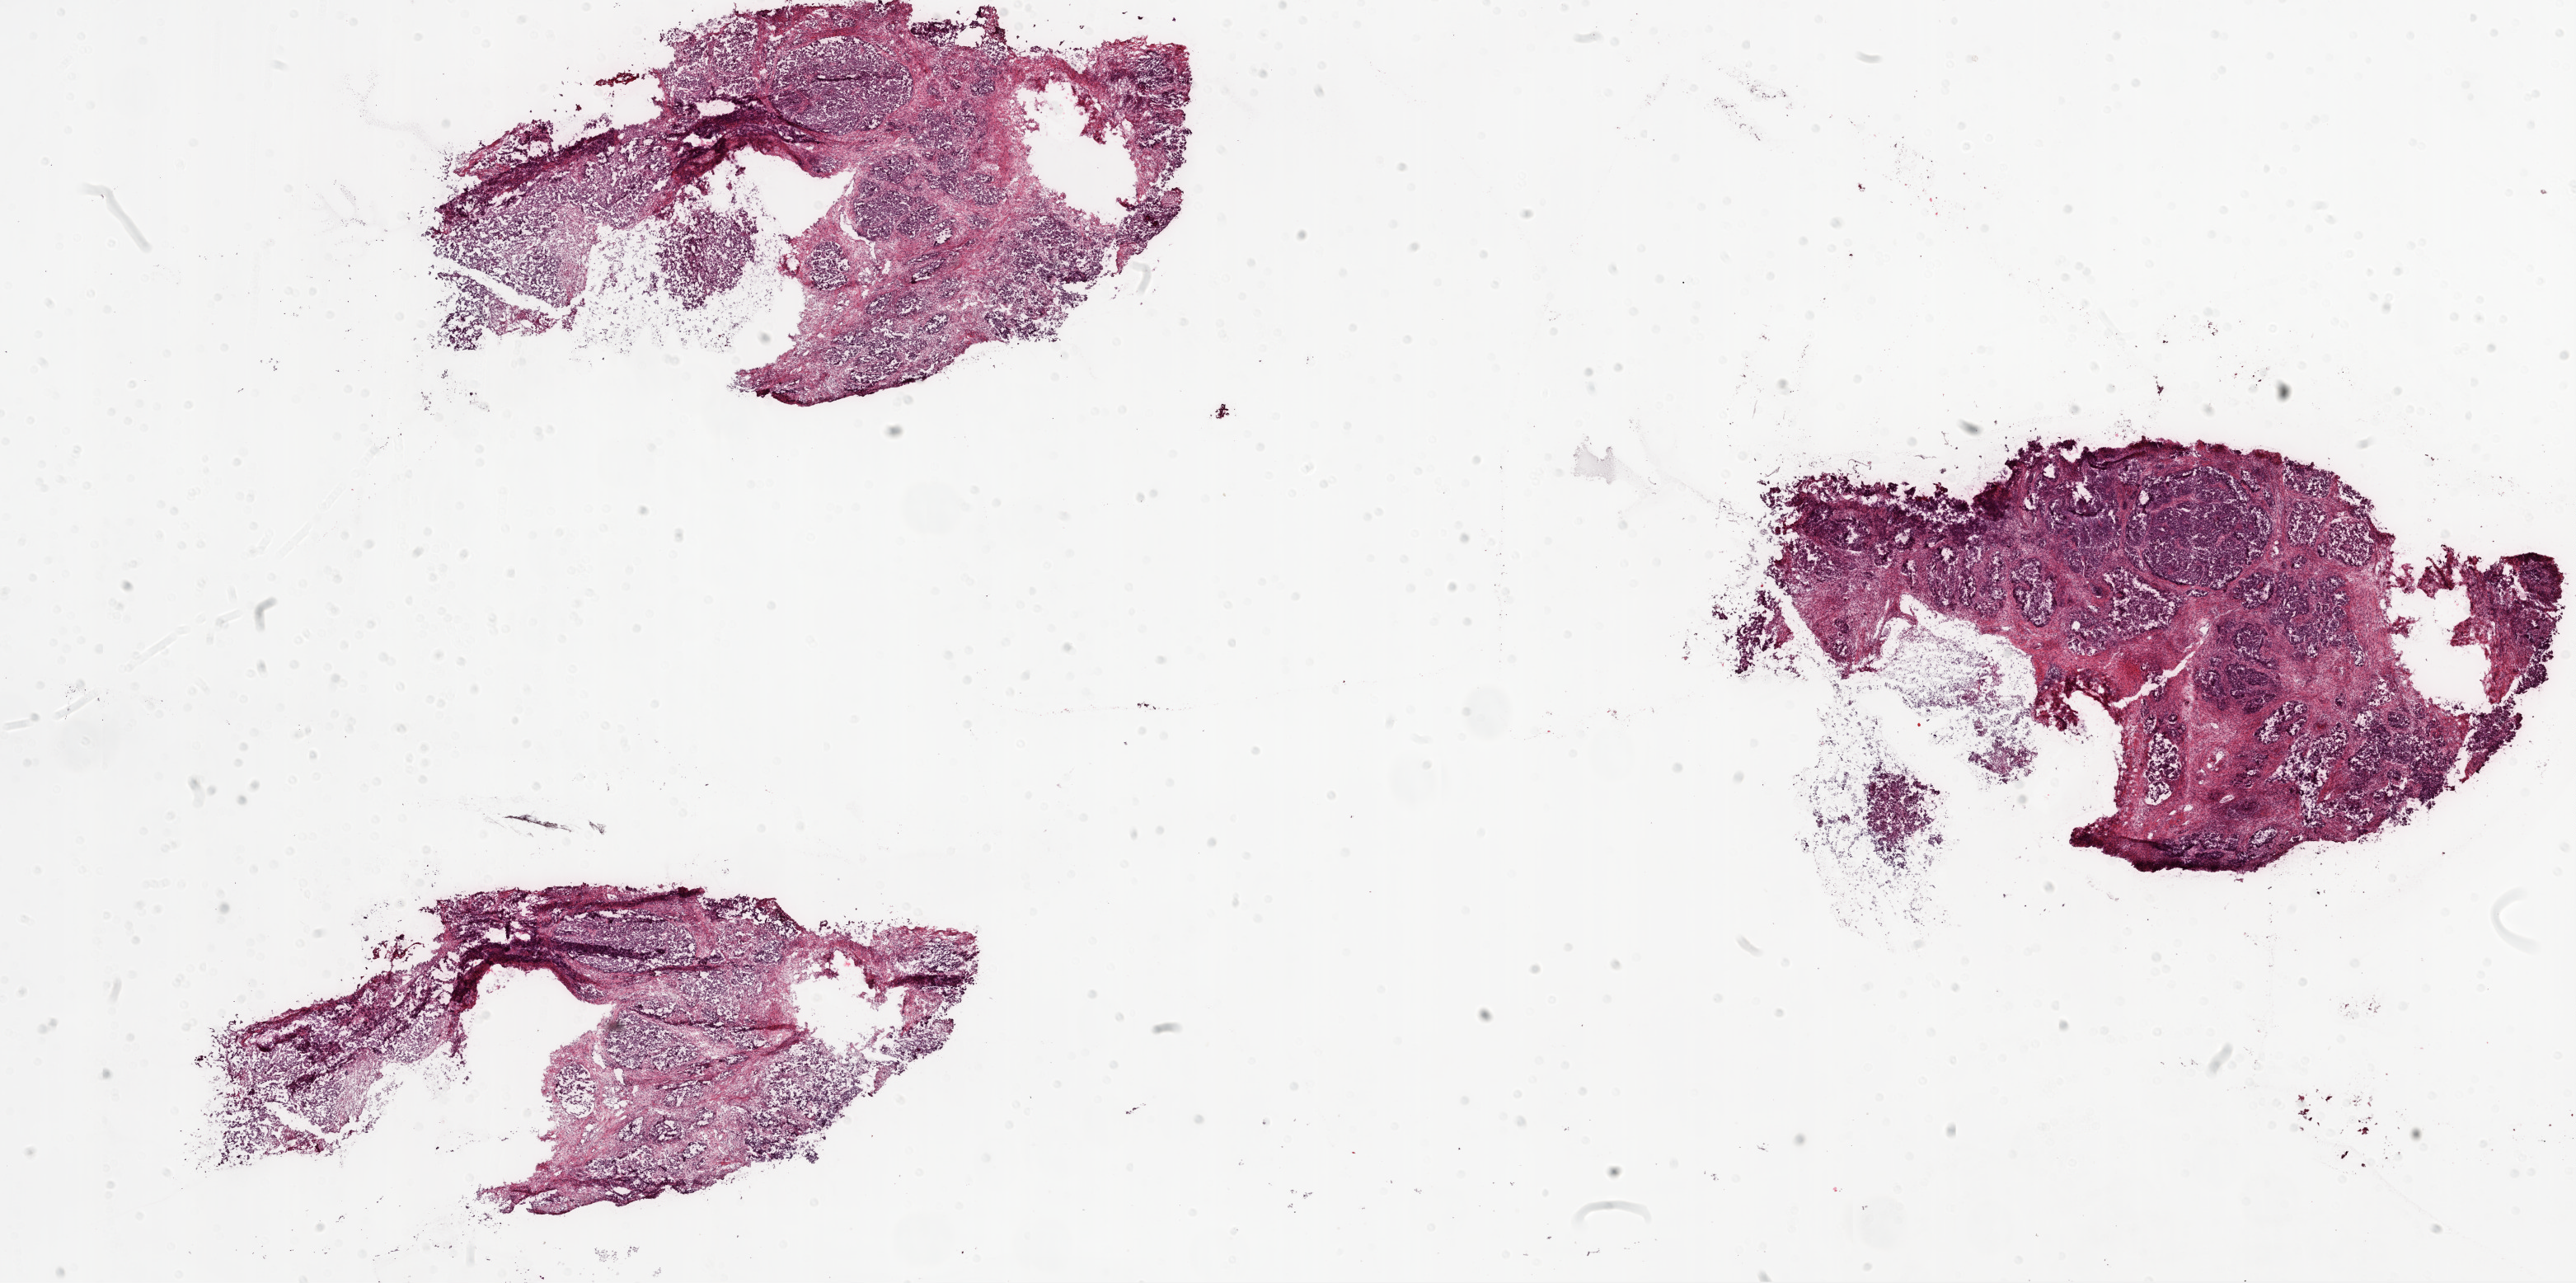
H&E whole-slide image — shown as a low-resolution overview of the whole scanned area (about 25.1 x 12.5 mm, acquisition: 20x scan); frozen section from the top of the tissue portion; primary tumour sample from the ovary. Female, age 61 years at initial diagnosis. Histologic grade: G3 (poorly differentiated). Pathologist review of this section (percent, as recorded): tumour cells 60%, tumour nuclei 70%, normal cells 0%, stromal cells 40%, necrosis 0%.
Pathologic diagnosis: Serous cystadenocarcinoma, NOS. FIGO stage: IIIC.